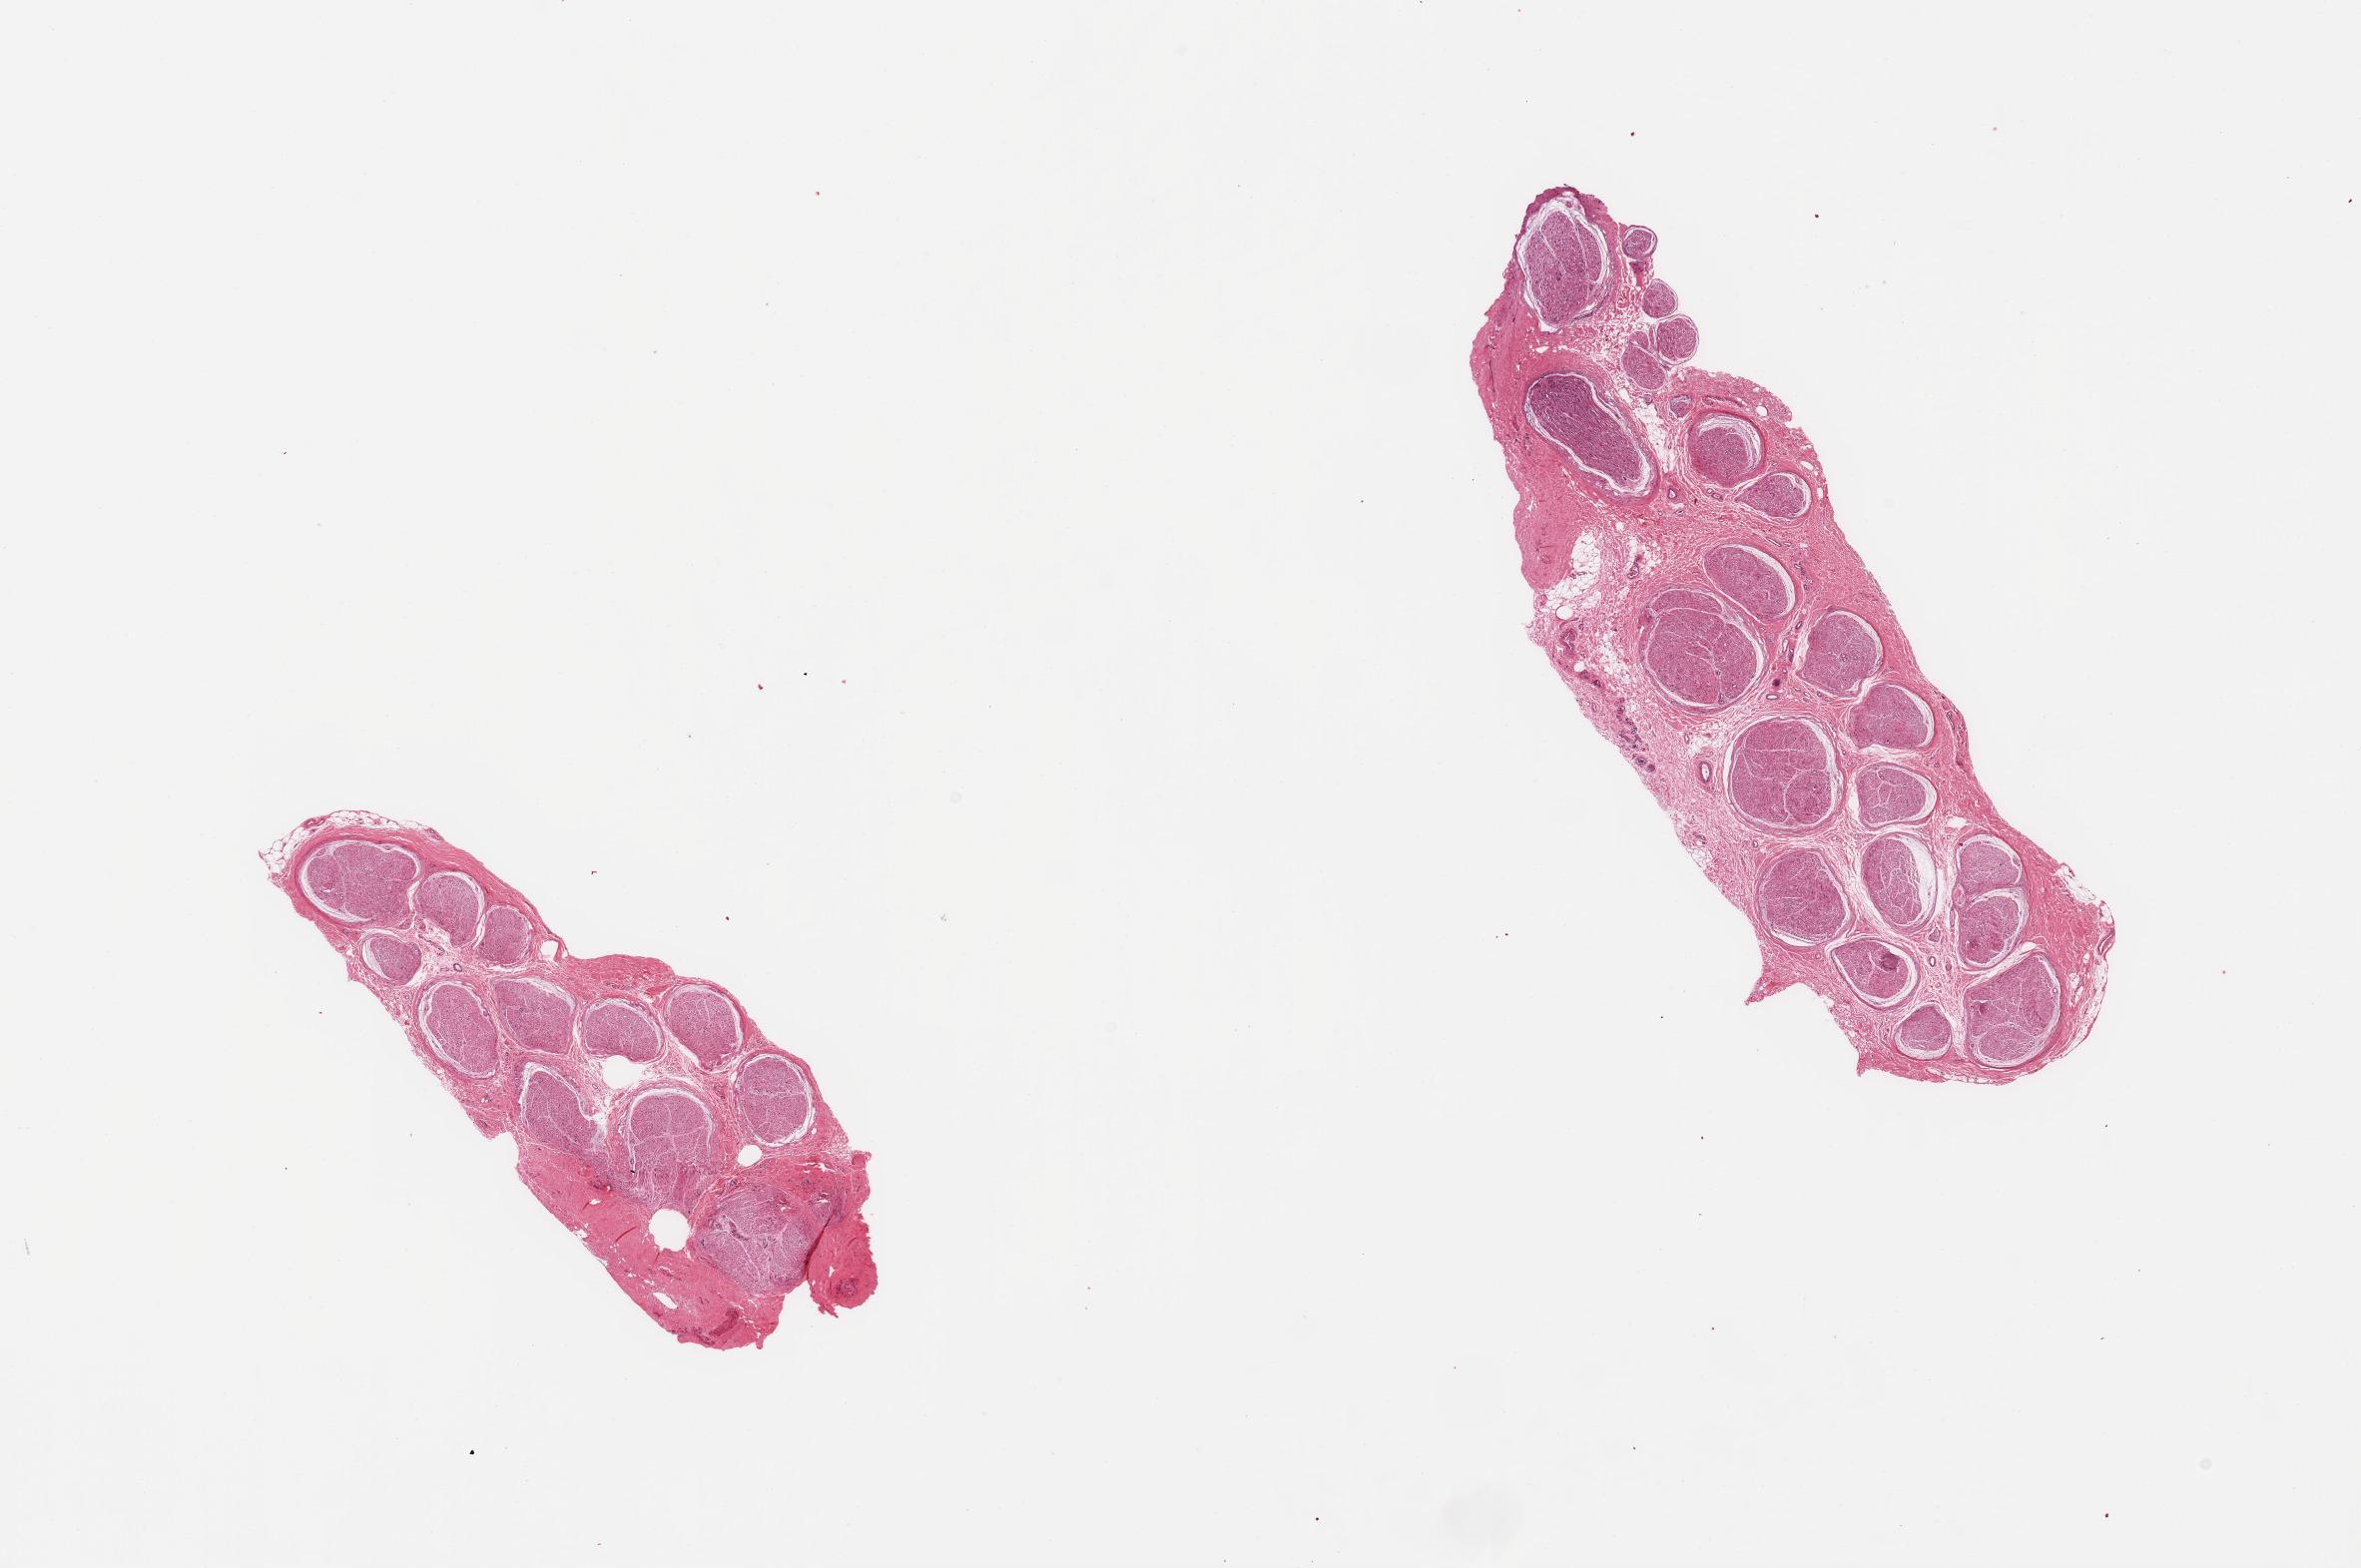
Whole-slide image, H&E stain — shown as a low-resolution overview of the whole scanned area (about 18.7 x 12.4 mm, acquisition: 20x scan), PAXgene-fixed, paraffin-embedded tissue, target tissue: tibial nerve, tissue donor sample. Donor sex: female.
Reviewer comment on this tissue sample: 2 pieces; well trimmed; 30% internal fibrous content.